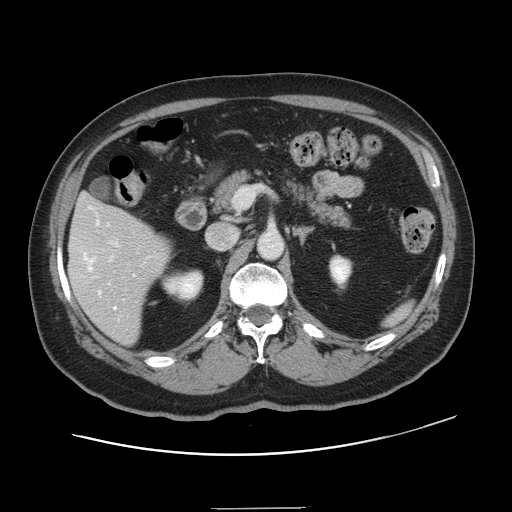
Contrast-enhanced abdominal CT, one axial slice. Slice 73 of 143 in the series (ordered by position). 120 kVp. Intravenous contrast given. Soft-tissue window (W 400 / L 40 HU). 2.5 mm slice thickness. 512 × 512 image matrix, field of view 402 × 402 mm. Male patient, age 62 years. Case-level facts recorded for this patient, not image findings: diagnosis: colorectal cancer liver metastases, imaged before liver resection; multiple liver metastases: yes; largest metastasis: 2.7 cm; disease in both lobes: no.
Outlined on this slice (manually delineated by an expert):
- hepatic veins: box from (x=84, y=206) to (x=135, y=320) px
- liver: (x=69, y=195)–(x=170, y=344)
- planned liver remnant (the part of the liver to remain after resection): (x=74, y=196)–(x=127, y=223)
- portal vein (with intrahepatic branches): (x=110, y=241)–(x=118, y=261)